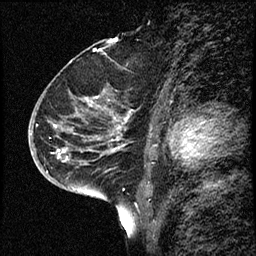
Breast MRI (dynamic contrast-enhanced), one sagittal slice; position 39 of 68 along the scan axis; dynamic contrast-enhanced study with each time point stored as its own series, time point 2 of 3 at this slice position (early post-contrast, ordered by acquisition time); 1.5 T; TE 4.2 ms, TR 17.6 ms; 256 × 256 image matrix, field of view 200 × 200 mm. Patient: female, 52 years. From the clinical record (not read from this slice): setting: breast cancer imaged before/during neoadjuvant chemotherapy; receptor status: HER2-positive.
Outlined on this slice (semi-automatically segmented with operator editing):
- analysis volume of interest (the breast-tissue region the enhancement analysis was run in; not a lesion): bounding box <50,61,144,184> (left, top, right, bottom; pixels)
- tumour enhancement mask (voxels above the 100 % enhancement threshold inside the analysis volume of interest): <61,101,120,153>